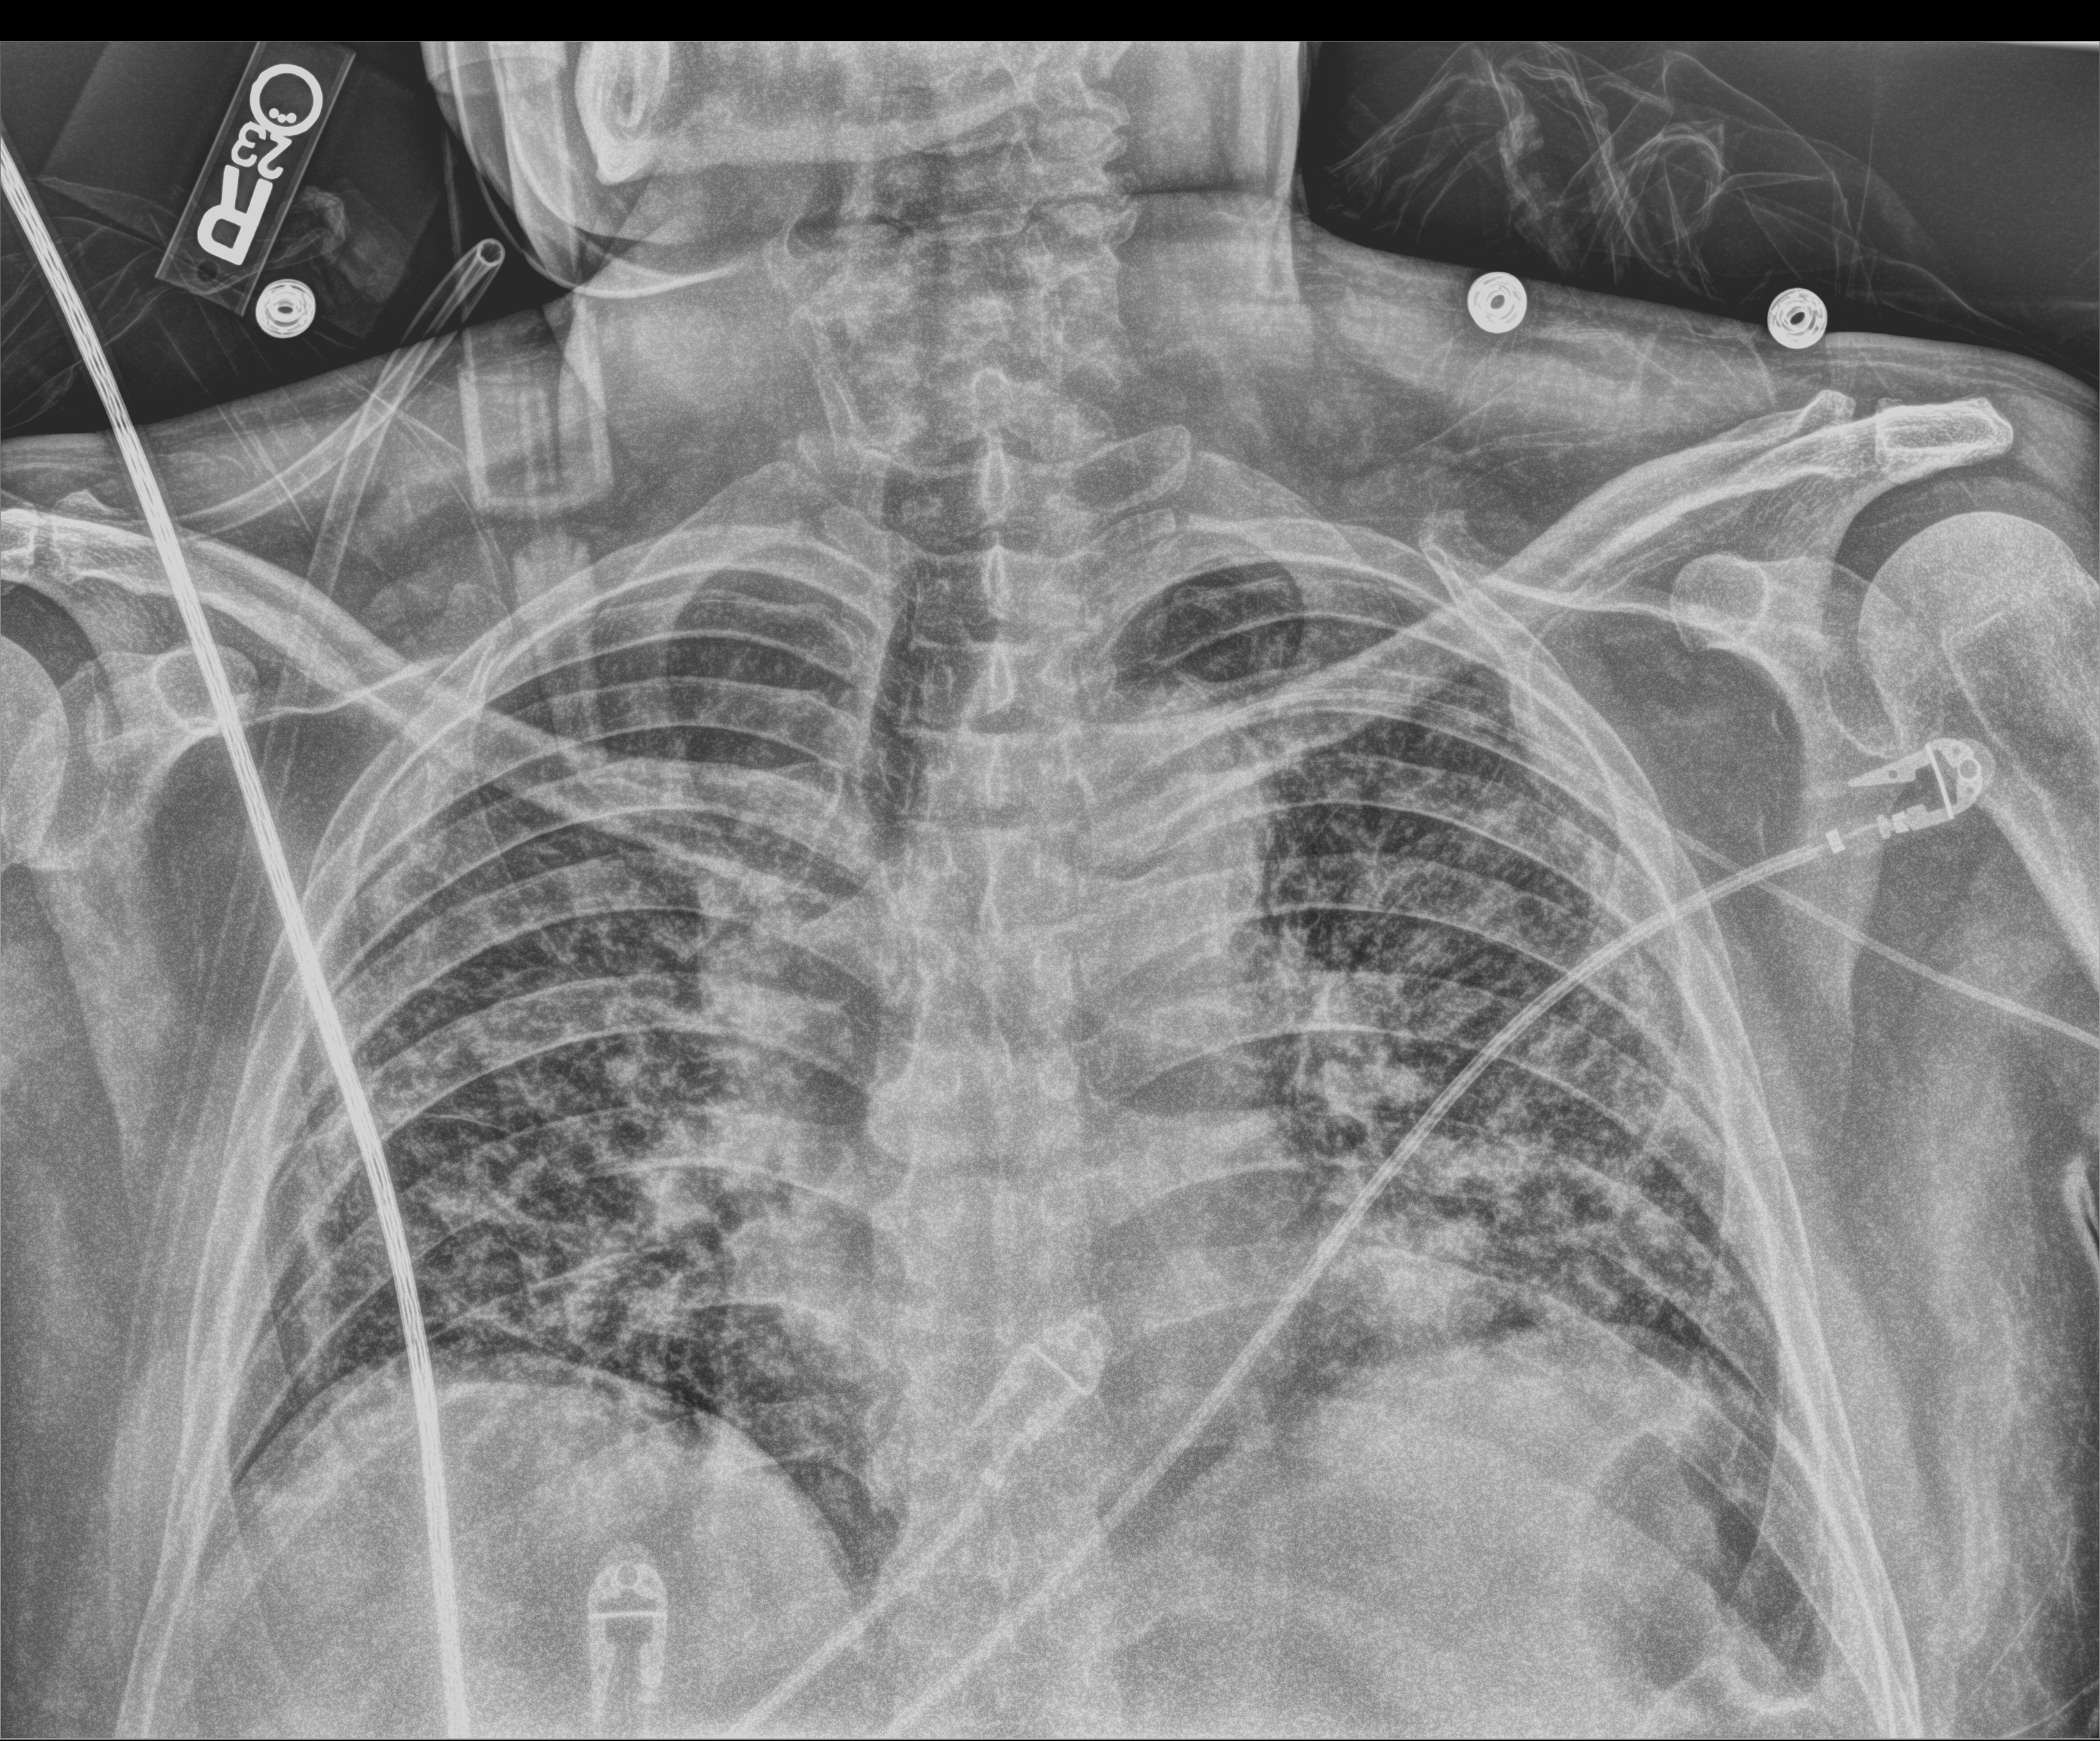
Portable chest radiograph; anteroposterior (AP) projection. Male patient hospitalised with COVID-19, age 60–74 years.
Hospital-stay facts (about this admission, not read from this image; timing relative to this image not recorded): hypertension (admission record): yes.